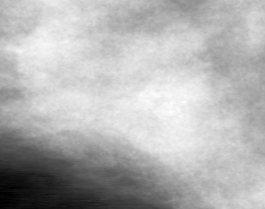
Crop from a digitized film mammogram around one marked abnormality; right breast; MLO view.
- Mass, shape lobulated, margins obscured; BI-RADS assessment category 0 (incomplete: needs additional imaging); pathology (as recorded): benign.